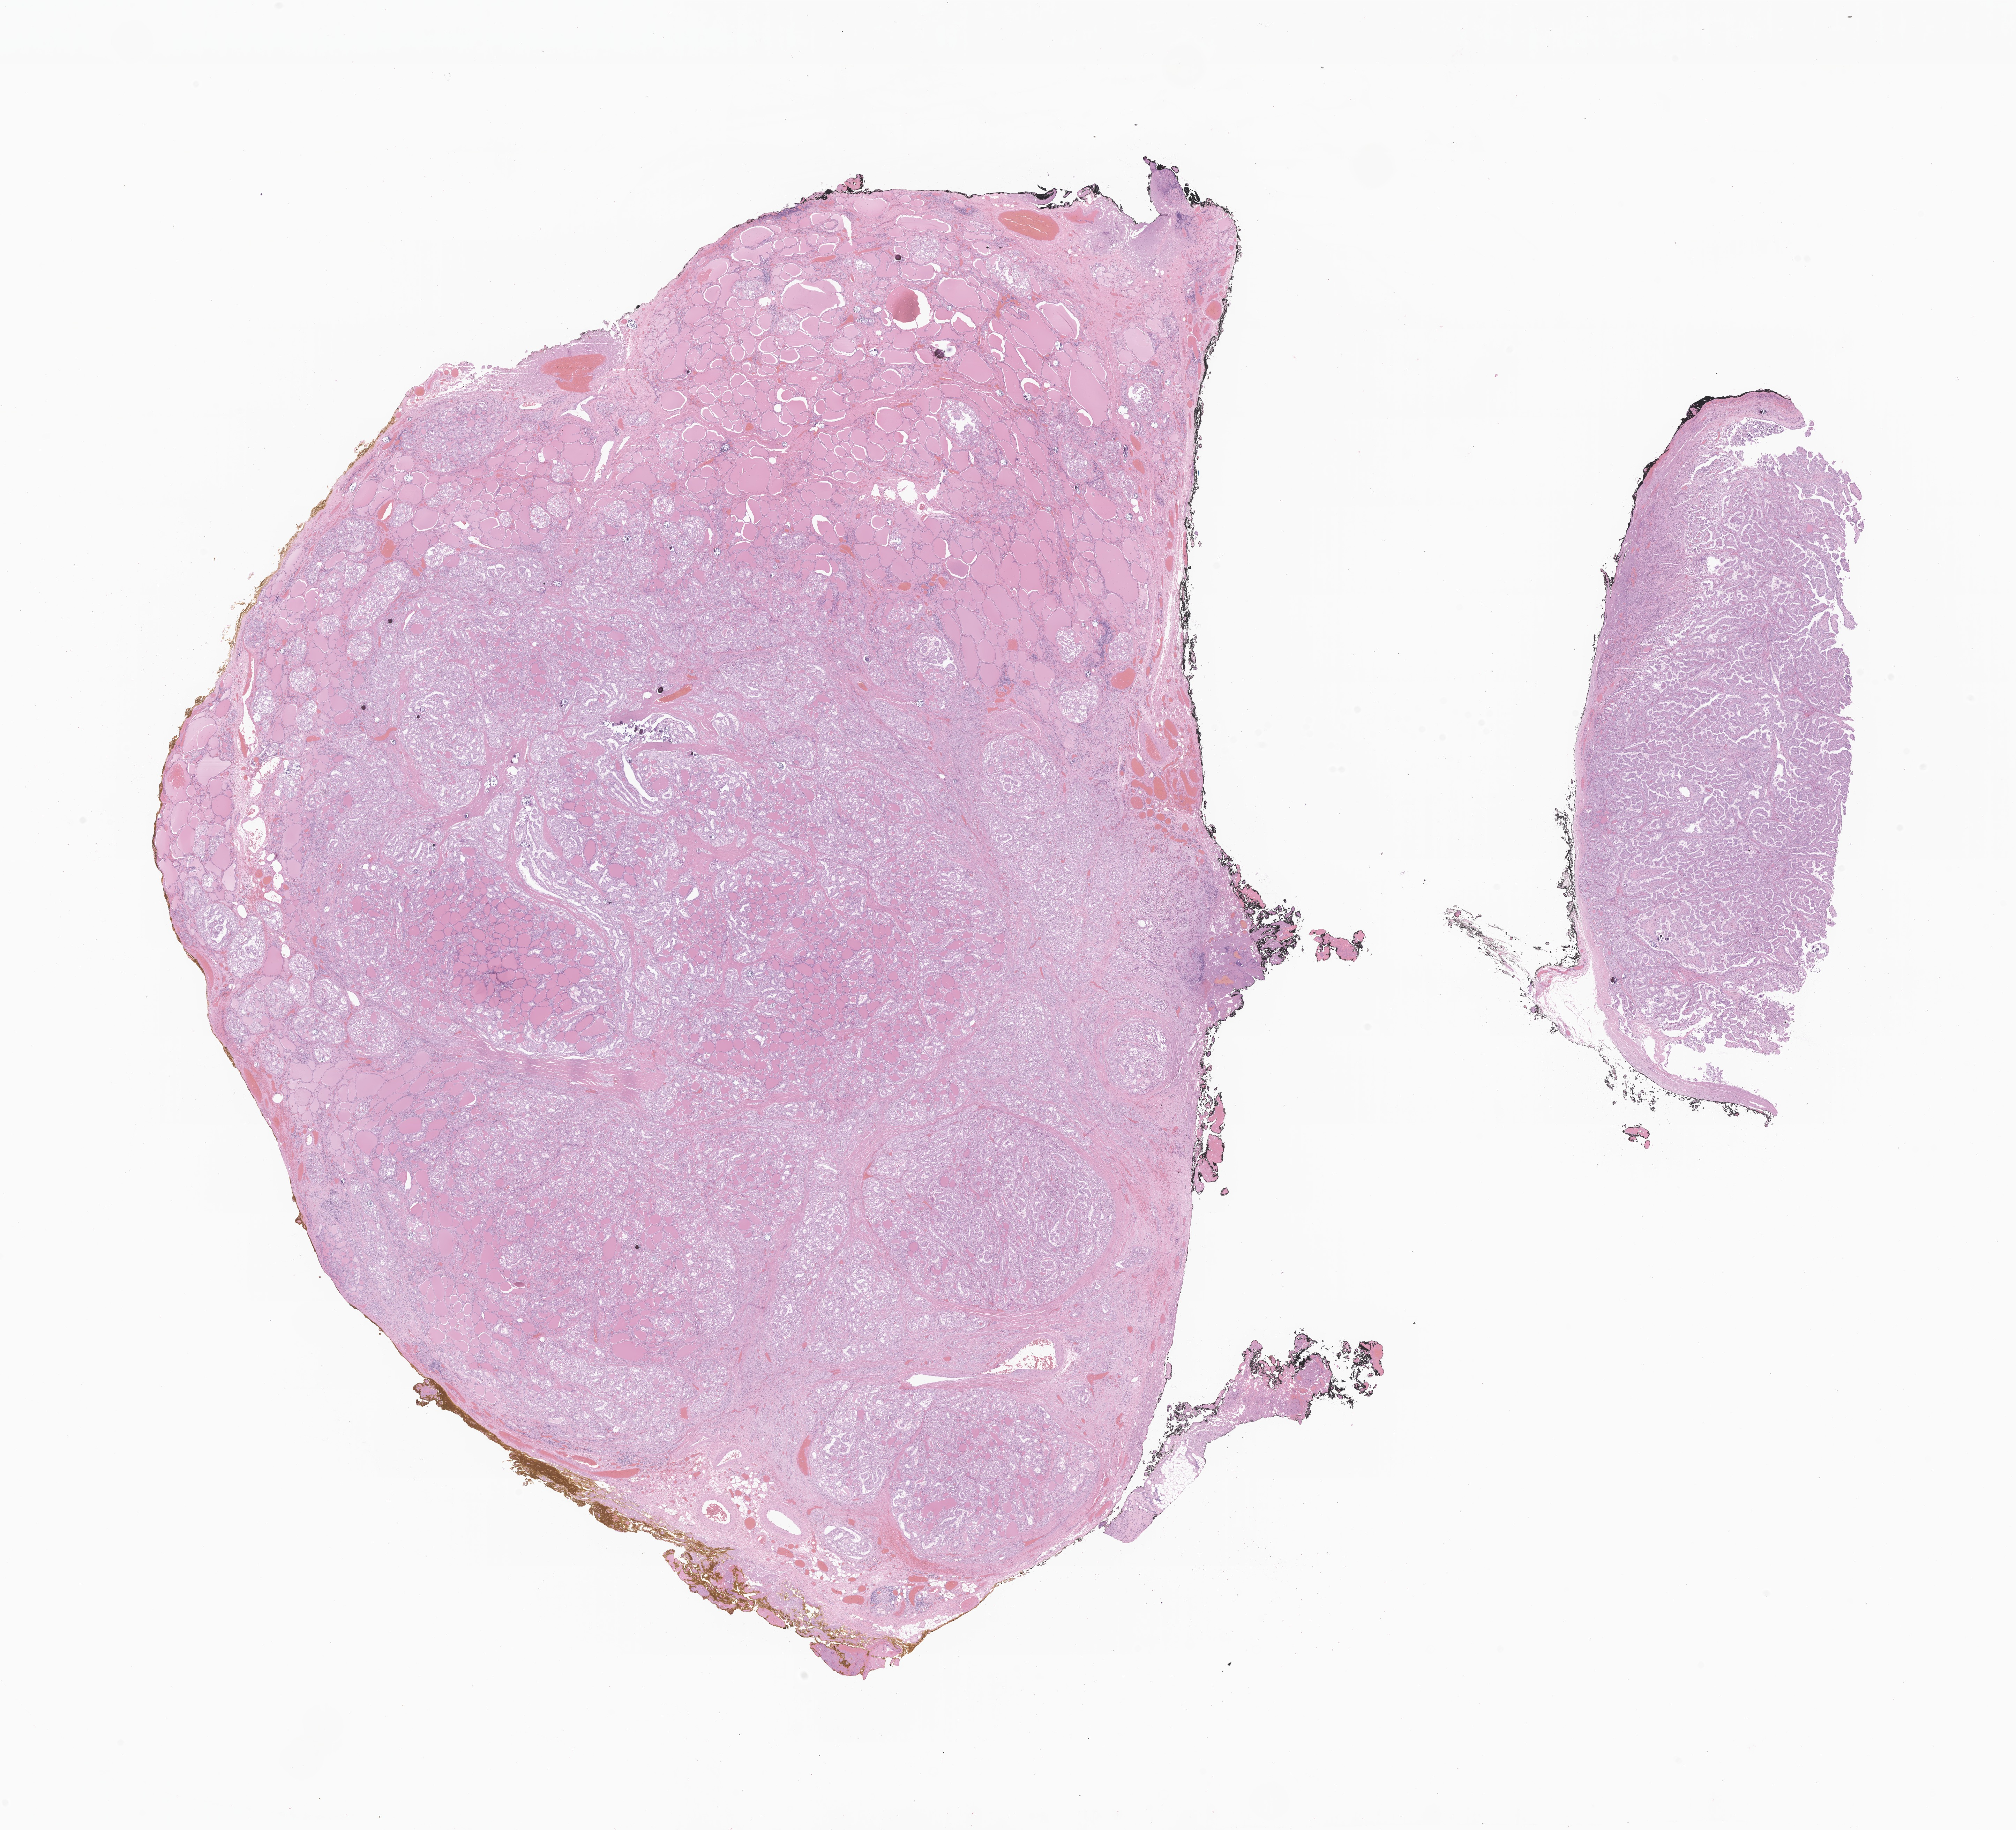
Whole-slide image, hematoxylin and eosin (H&E) stain of tumor tissue from the thyroid — low-resolution overview of the scanned area, about 24.4 x 22.1 mm; FFPE section. Female patient, age 161 months (13 years 5 months).
- diagnosis: Papillary carcinoma, NOS